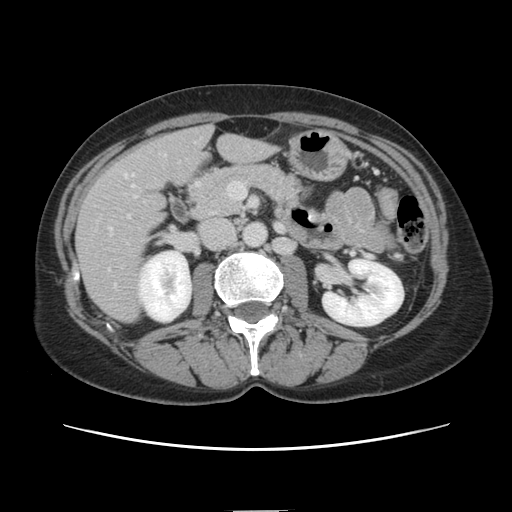
Contrast-enhanced abdominal CT, one axial slice. Slice 52 of 141 in the series (ordered by position). 120 kVp. Intravenous contrast given. Soft-tissue window (W 400 / L 40 HU). 512 × 512 image matrix. Female patient, age 63 years. From the clinical record (not read from this slice): diagnosis: colorectal cancer liver metastases, imaged before liver resection; multiple liver metastases: yes; largest metastasis: 3.2 cm; disease in both lobes: yes.
Outlined on this slice (manually delineated by an expert):
- liver: bounding box <77,127,272,322> (left, top, right, bottom; pixels)
- planned liver remnant (the part of the liver to remain after resection): <178,128,272,176>
- portal vein (with intrahepatic branches): <110,174,132,230>